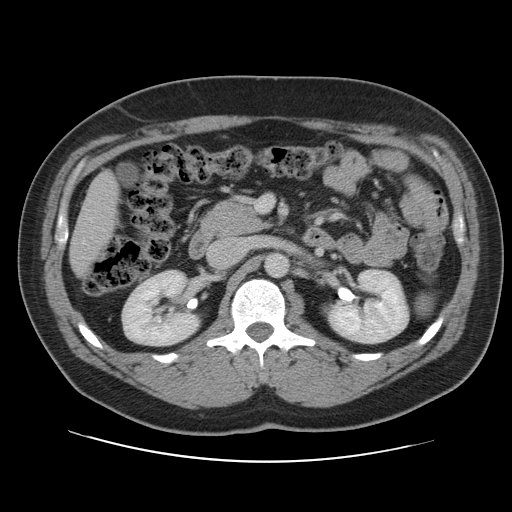
Contrast-enhanced abdominal CT, one axial slice; slice 51 of 109 in the series (ordered by position); 120 kVp; intravenous contrast given; soft-tissue window (W 400 / L 40 HU); 512 × 512 image matrix. Male patient, age 35 years. From the clinical record (not read from this slice): diagnosis: colorectal cancer liver metastases, imaged before liver resection; multiple liver metastases: yes; largest metastasis: 2.8 cm; disease in both lobes: yes.
Annotated regions visible in this slice (outlined manually by an expert reader):
- liver: bounding box <71,174,118,272> (left, top, right, bottom; pixels)
- planned liver remnant (the part of the liver to remain after resection): <71,174,119,273>